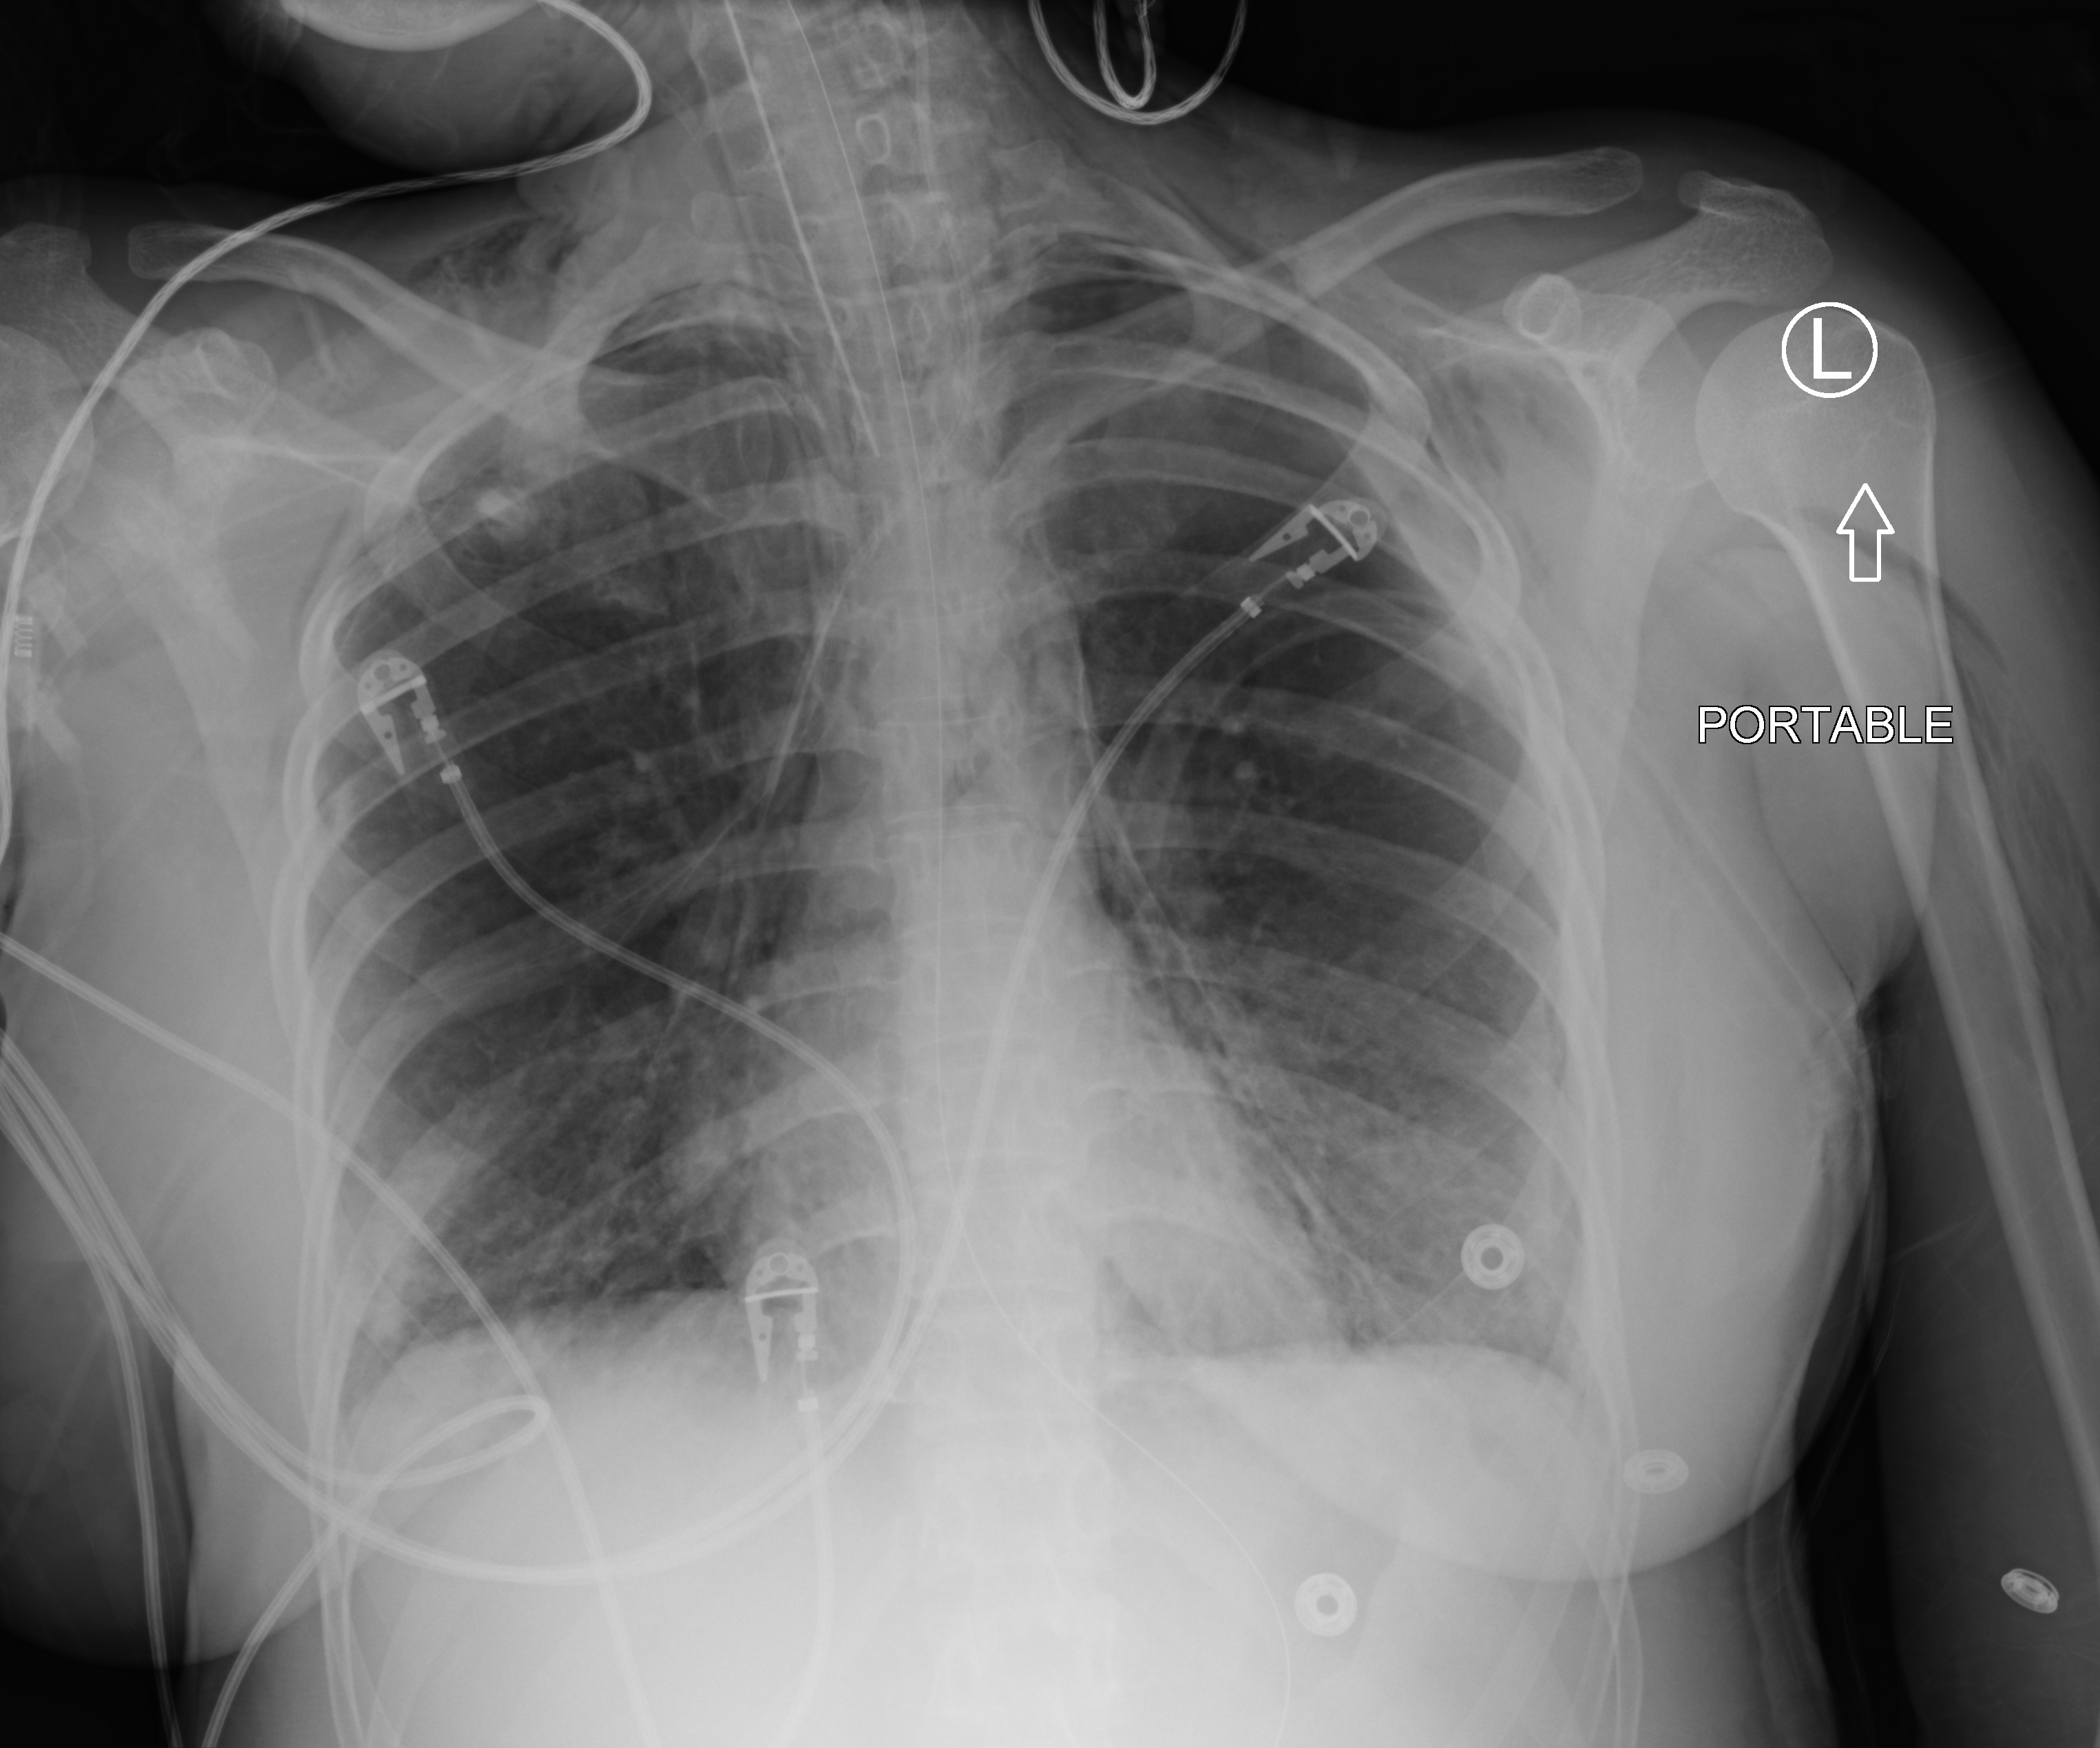
Bedside chest radiograph (computed radiography), anteroposterior (AP) projection. Patient hospitalised with COVID-19, aged 18–59 years.
Admission-level facts for this patient (not findings on this image; timing relative to this image not recorded): length of hospital stay: 30 days; admitted to intensive care during this hospital stay: yes; hypertension (admission record): no.